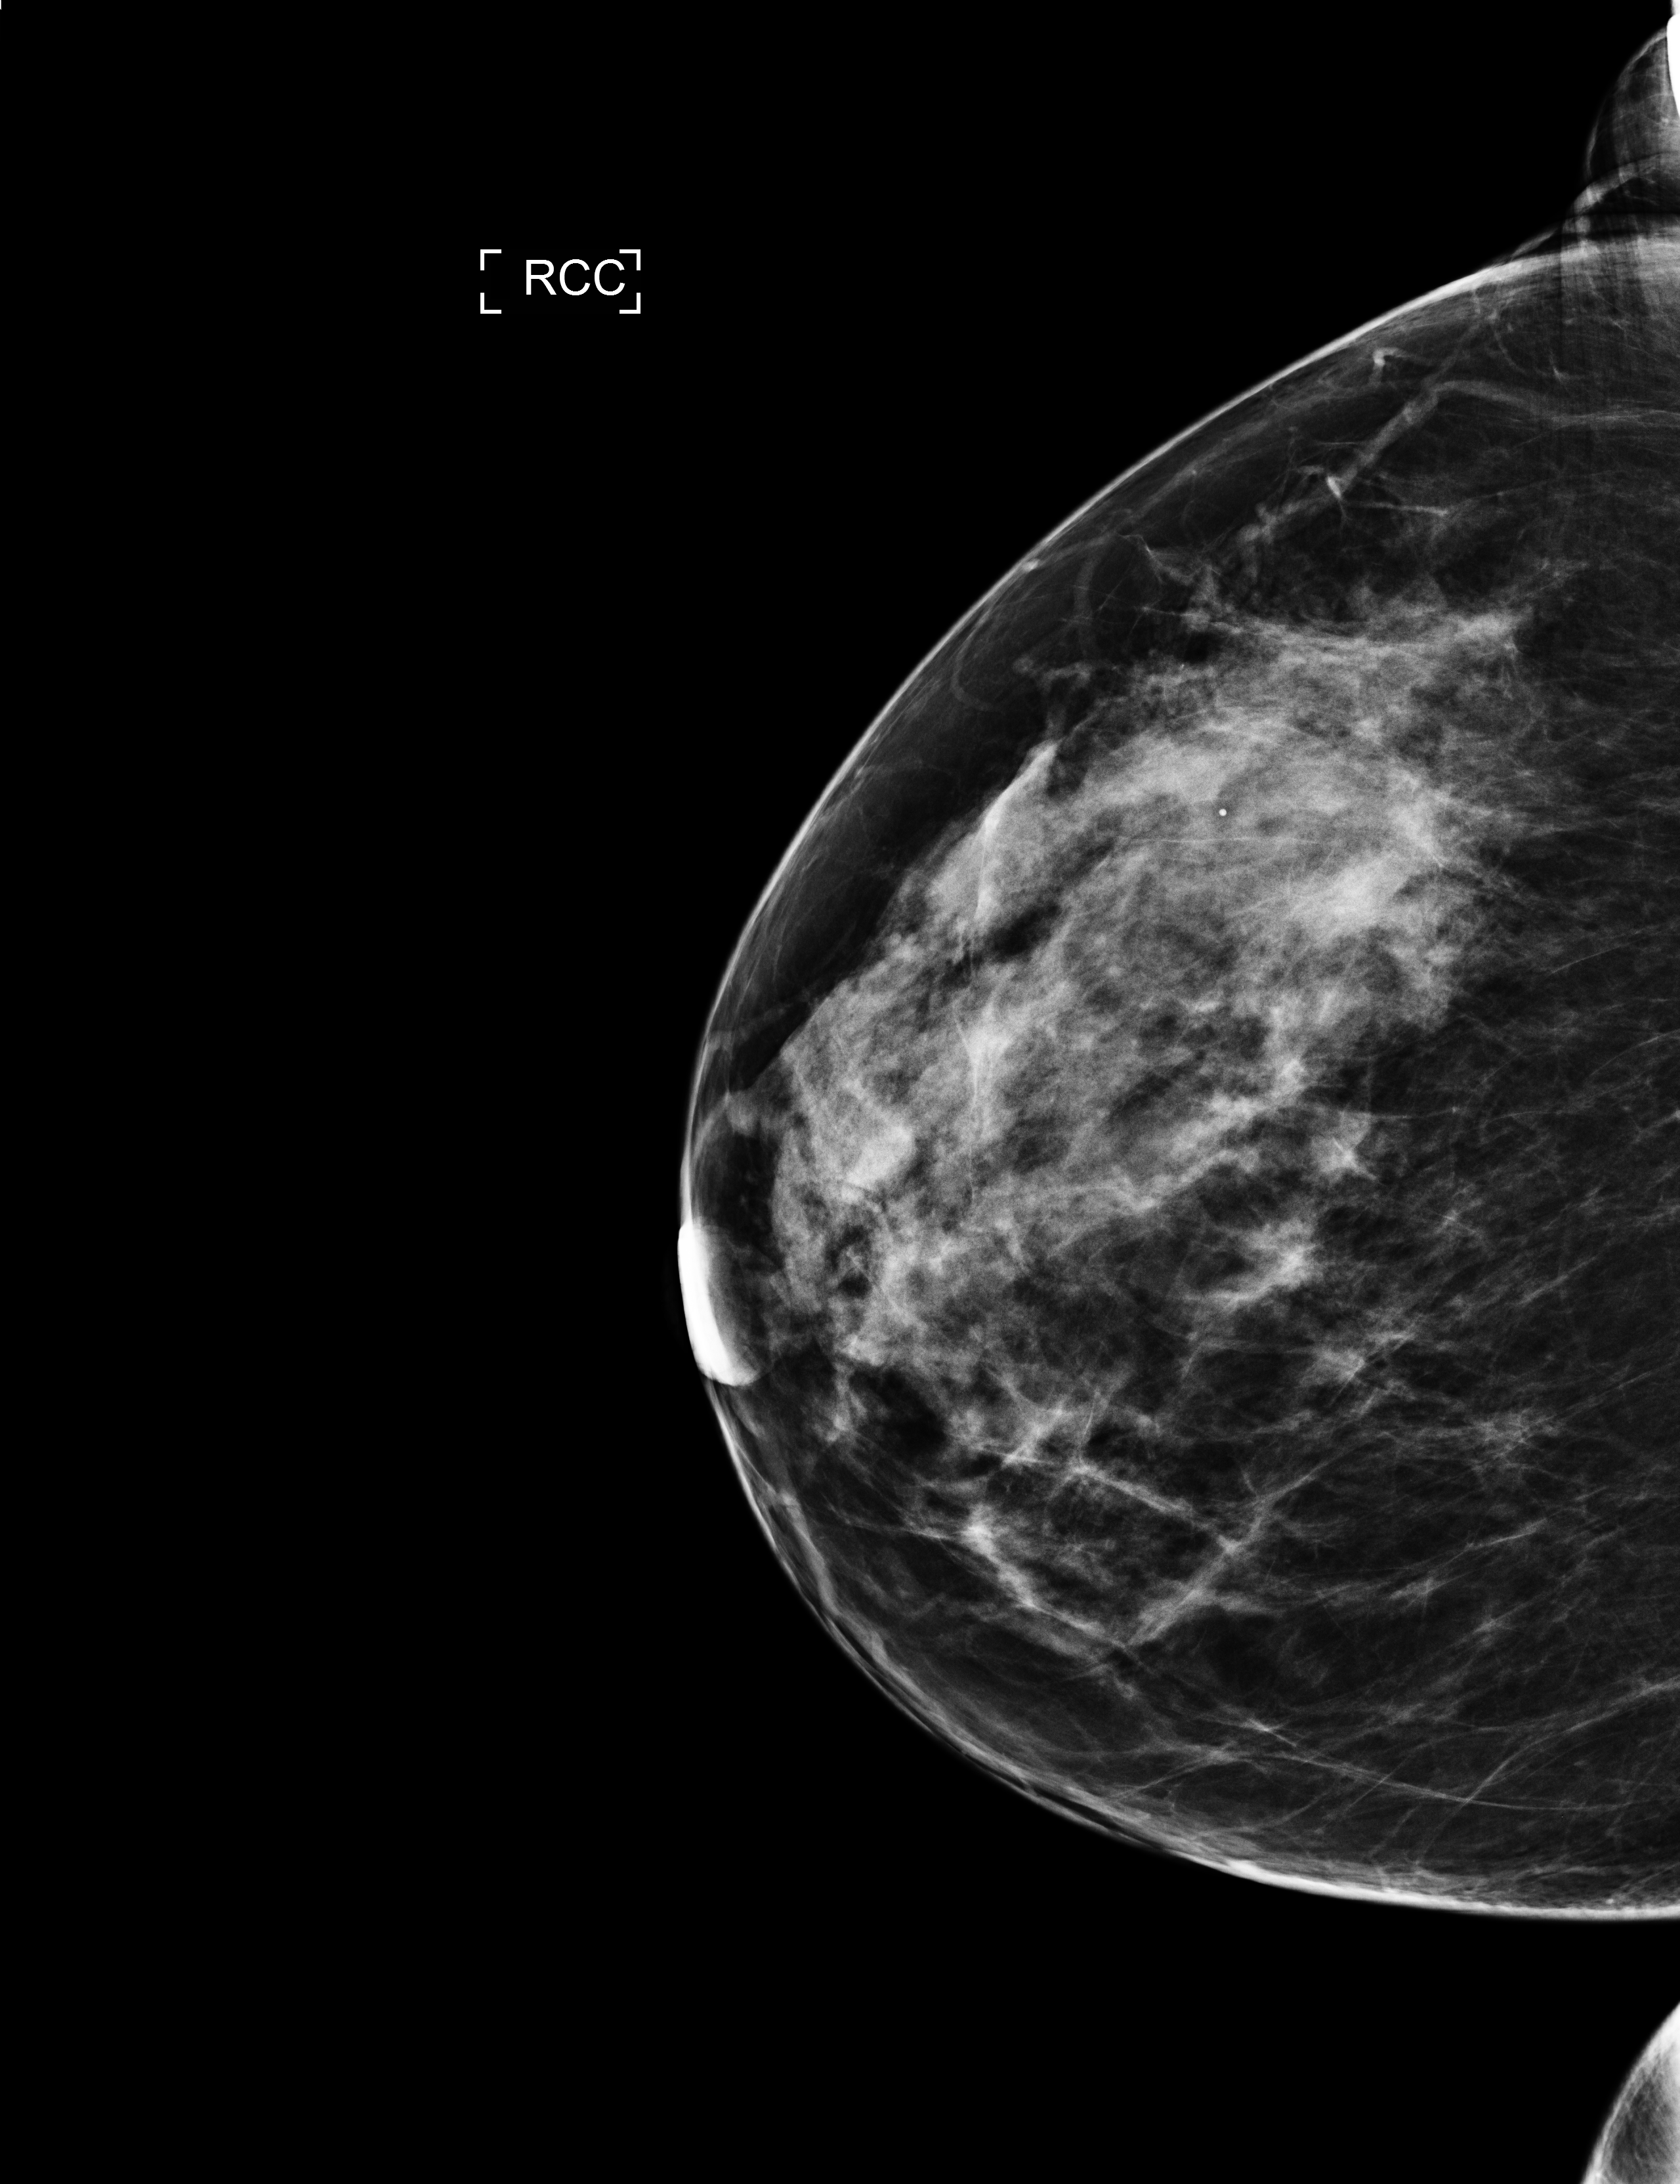
Digital mammogram (FFDM); right breast; cranio-caudal projection; screening examination; system: Selenia Dimensions. Patient: female, 41 years.
Final BI-RADS category for the screening round (tomosynthesis exam, both breasts): category 1.